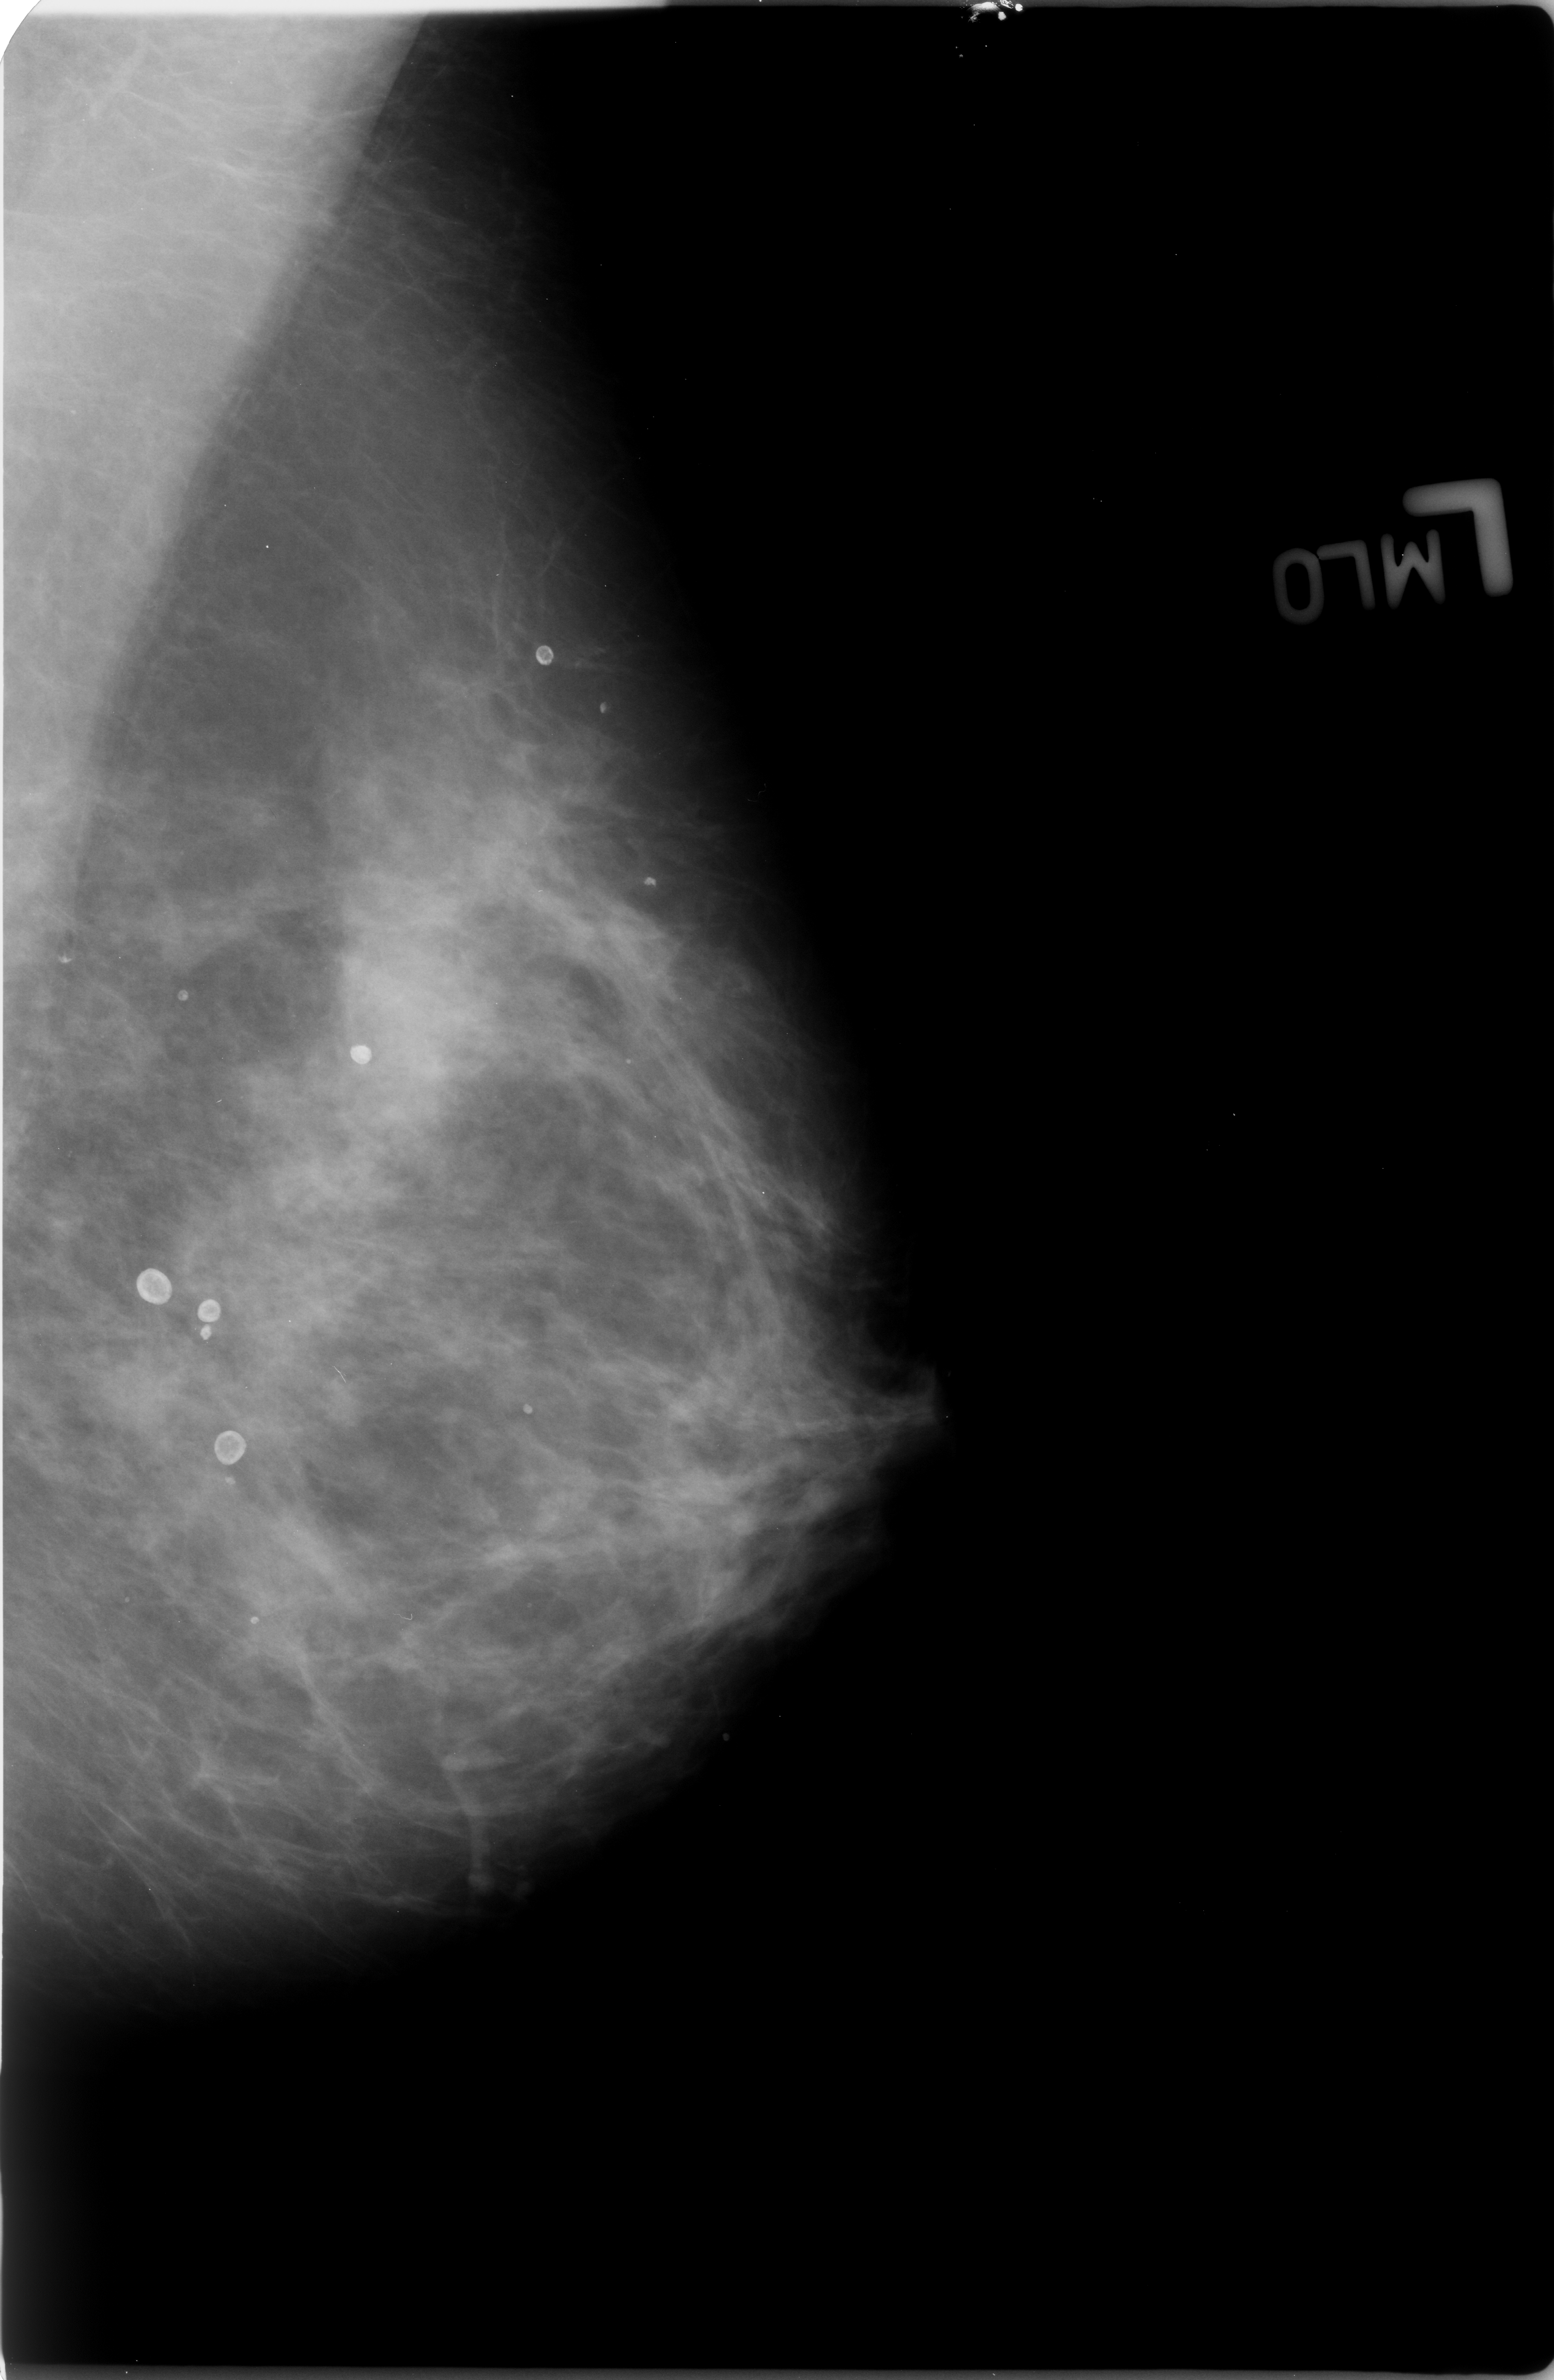
Scanned film-screen mammogram; left breast; MLO view; 1554 × 2380 image matrix.
Expert-marked regions of interest on this image (one box per marked abnormality):
- Finding 1 of 6: calcifications, morphology round and regular / eggshell; BI-RADS assessment category 2; subtlety rating 3 on a 1 (subtle) to 5 (obvious) scale; benign; no additional work-up was recommended (outcome (as recorded, no biopsy): benign without callback): bounding box (x1, y1, x2, y2) in pixels: (111, 1247, 191, 1315)
- Finding 2 of 6: calcifications, morphology round and regular / eggshell; BI-RADS assessment category 2; benign; no additional work-up was recommended (outcome (as recorded, no biopsy): benign without callback): (173, 1272, 241, 1344)
- Finding 3 of 6: calcifications, morphology round and regular / eggshell; BI-RADS assessment category 2; benign; no additional work-up was recommended (outcome (as recorded, no biopsy): benign without callback): (181, 1408, 274, 1493)
- Finding 4 of 6: calcifications, morphology round and regular / eggshell; BI-RADS assessment category 2; outcome (as recorded, no biopsy): benign without callback (not worked up further): (314, 1011, 418, 1104)
- Finding 5 of 6: calcifications, morphology round and regular / eggshell; BI-RADS assessment category 2; subtlety rating 3 on a 1 (subtle) to 5 (obvious) scale; outcome (as recorded, no biopsy): benign without callback (not worked up further): (504, 607, 592, 708)
- Finding 6 of 6: calcifications, morphology round and regular / eggshell; BI-RADS assessment category 2; benign; no additional work-up was recommended (outcome (as recorded, no biopsy): benign without callback): (611, 859, 683, 927)